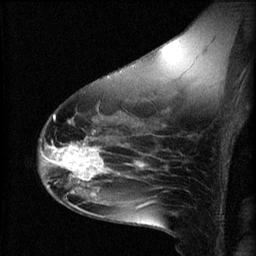
Breast MRI (dynamic contrast-enhanced), one sagittal slice. Position 37 of 60 along the scan axis. 3 images stored at this slice position (order not interpretable as contrast timing). 1.5 T. TE 4.2 ms, TR 8.2 ms. 256 × 256 image matrix, field of view 180 × 180 mm. Patient: female, 49 years.
Outlined on this slice (semi-automatic segmentation, software-assisted and operator-edited):
- analysis volume of interest (the breast-tissue region the enhancement analysis was run in; not a lesion): bounding box [x1, y1, x2, y2] px = [45, 136, 109, 187]
- tumour enhancement mask (voxels above the 70 % enhancement threshold inside the analysis volume of interest): [45, 142, 109, 187]